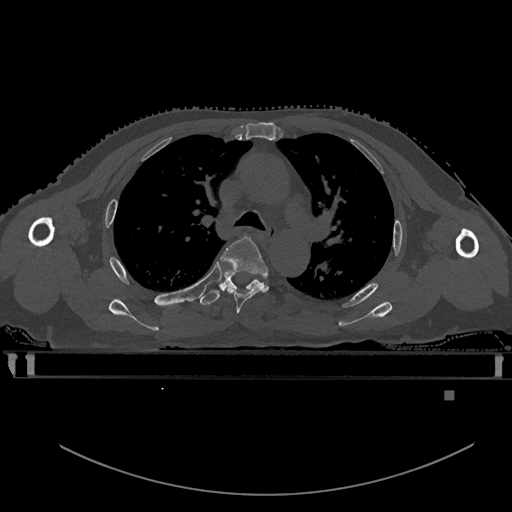
CT including the spine, one axial slice; slice 386 of 969 in the series (ordered by position); bone window (W 1800 / L 400 HU); 512 × 512 image matrix, field of view 456 × 456 mm. Patient: male, 82 years. Case-level facts recorded for this patient, not image findings: primary cancer: prostate.
Outlined on this slice (semi-automatic segmentation, software-assisted and operator-edited):
- T4 vertebra: bounding box (x1, y1, x2, y2) in pixels: (220, 236, 269, 313)
- T5 vertebra: (200, 272, 262, 306)